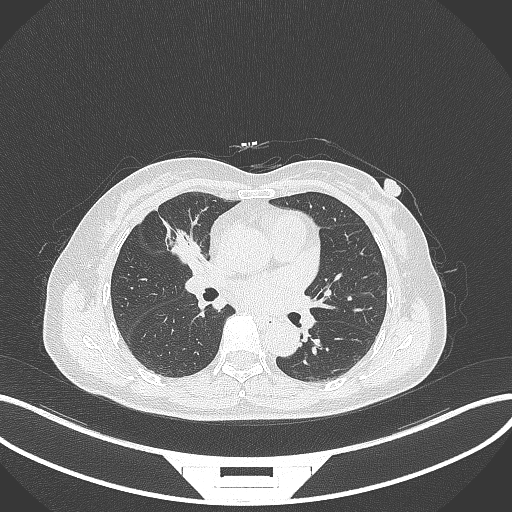
Chest CT, one axial slice. Slice 159 of 284 in the series (ordered by position). 120 kVp. Lung window (W 1500 / L -600 HU). 1 mm slice thickness. 512 × 512 image matrix, field of view 400 × 400 mm. Patient: female, 51 years. From the clinical record (not read from this slice): clinical TNM (as recorded): T1c N0 M0.
Structures marked on this image (bounding box drawn by a radiologist):
- lung tumour (recorded histology: adenocarcinoma): bounding box (x1, y1, x2, y2) in pixels: (165, 224, 206, 270)